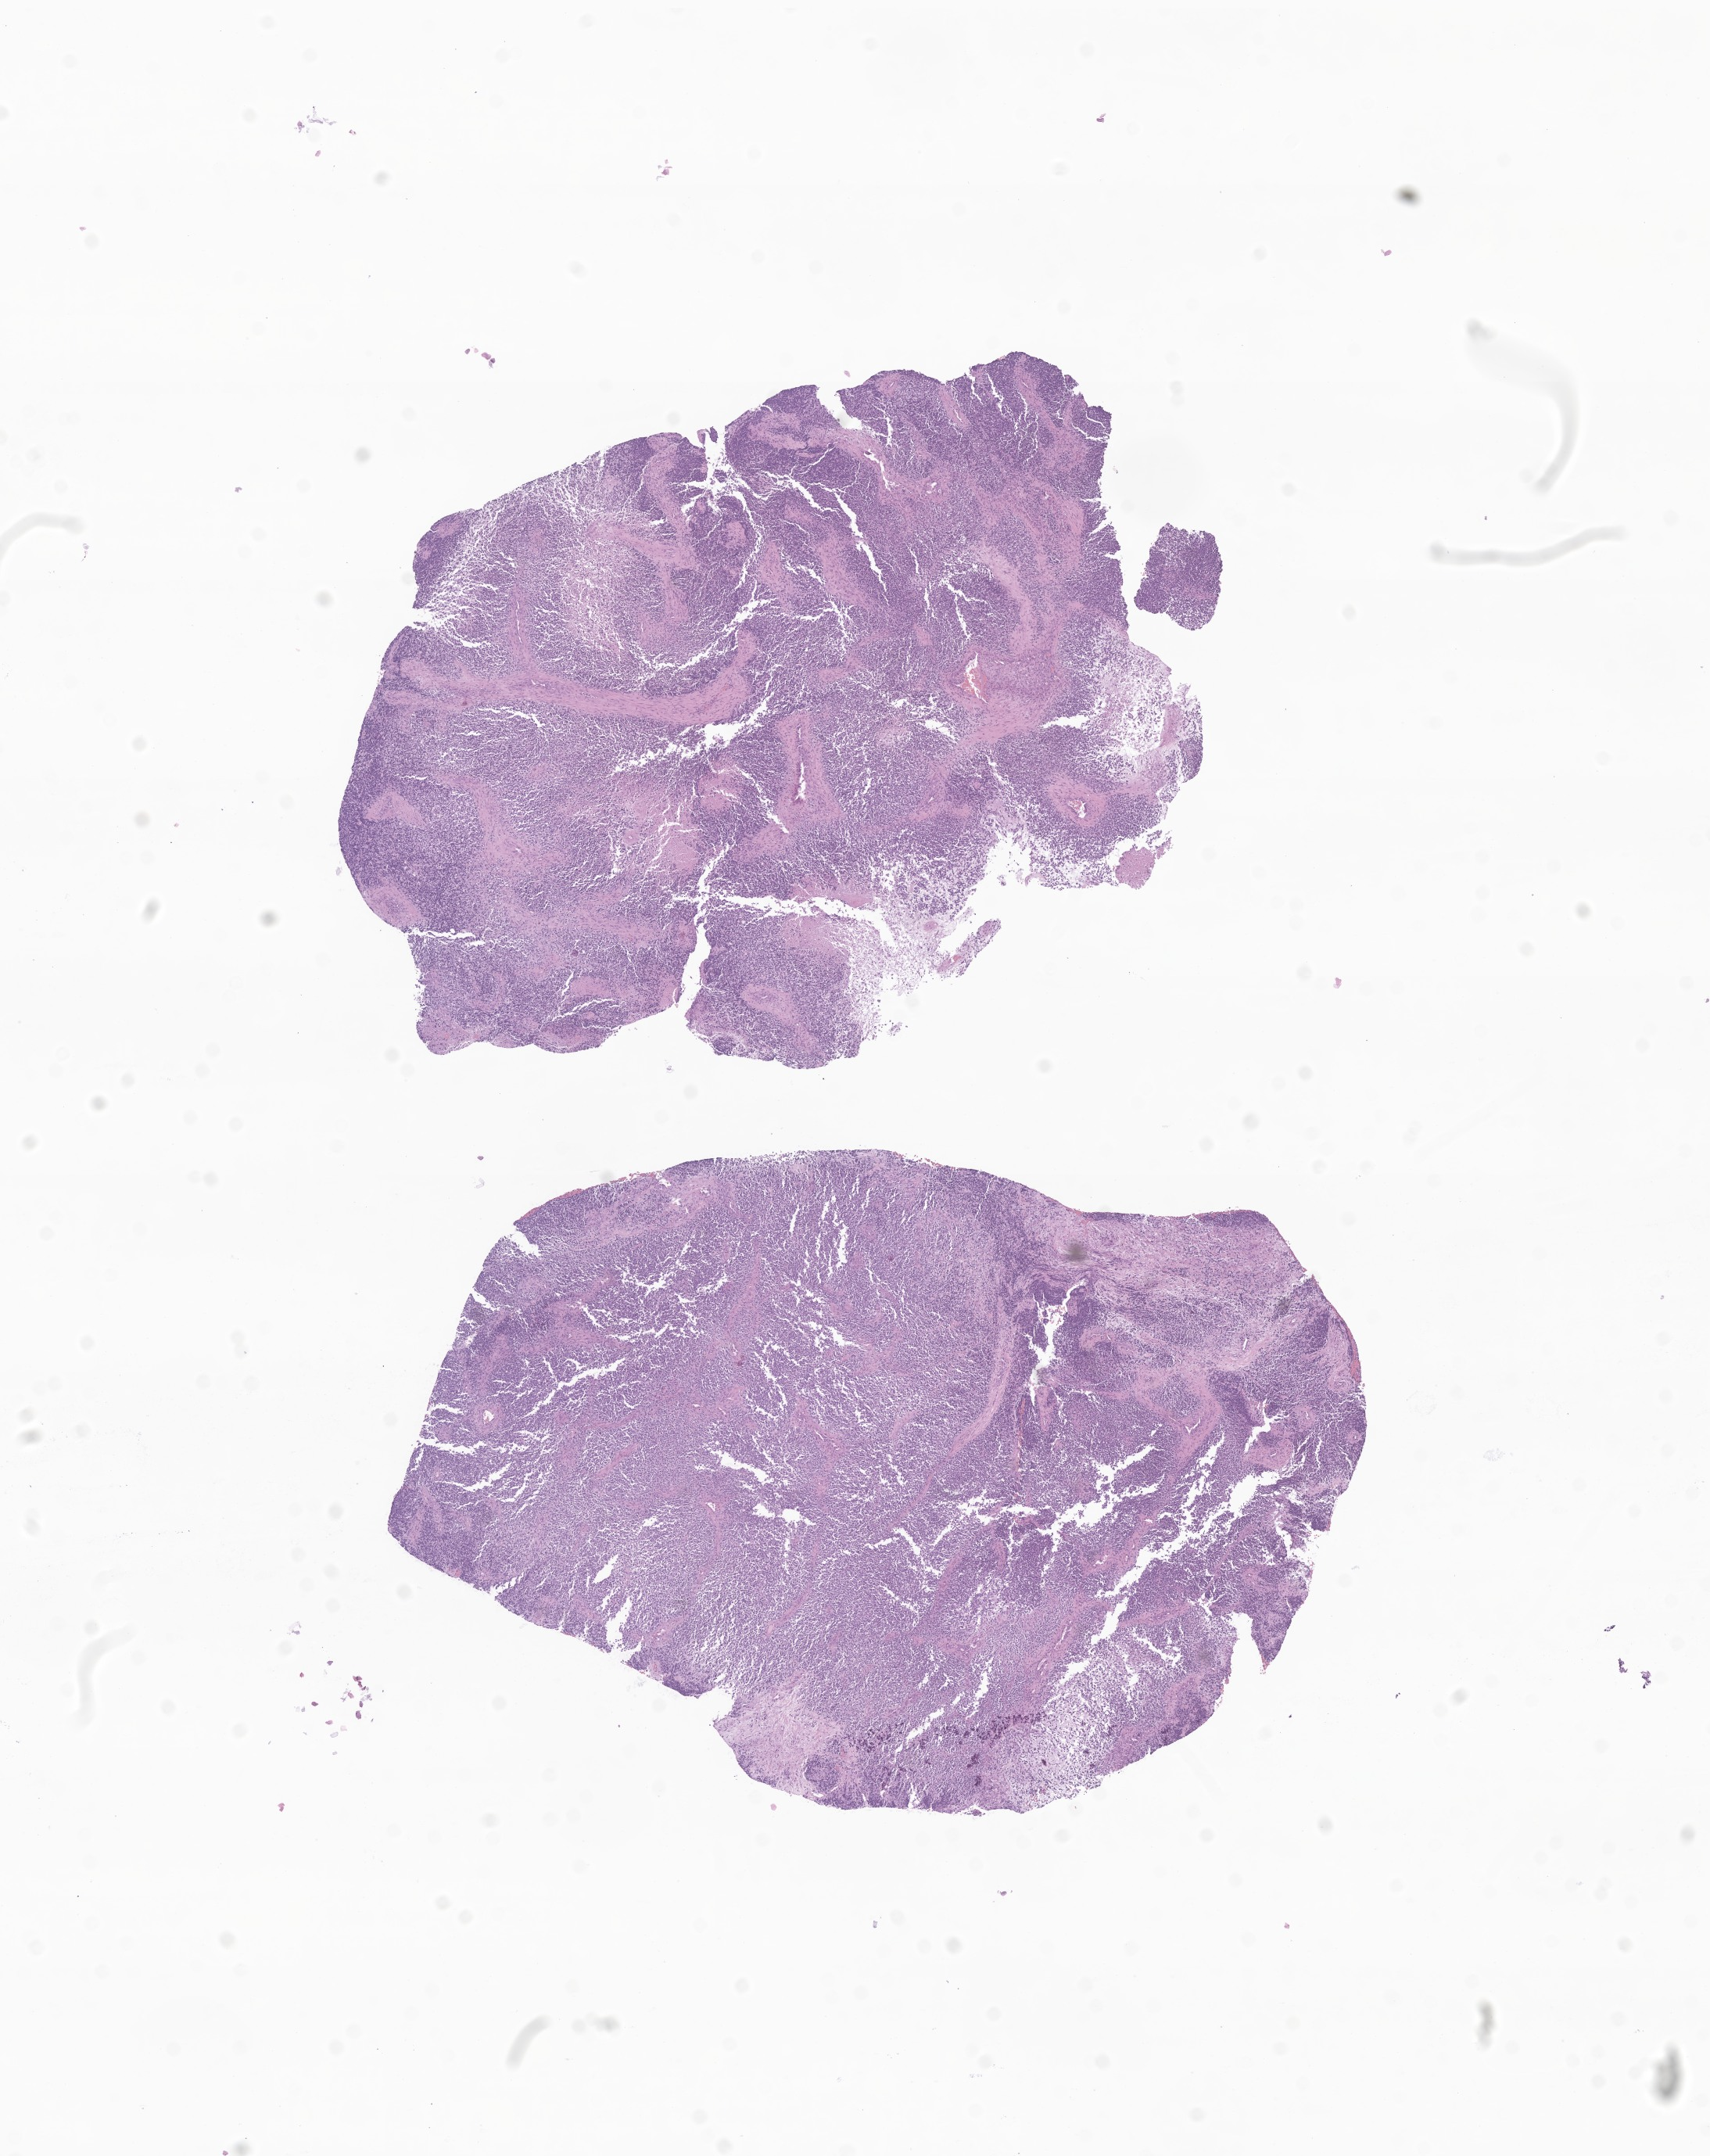
Whole-slide image, haematoxylin and eosin stain of tumor tissue from the orbit — low-resolution overview of the scanned area, about 9.2 x 11.6 mm. Formalin-fixed, paraffin-embedded (FFPE) tissue. Male patient, age 70 months (5 years 10 months).
Recorded diagnosis: Rhabdomyoma, NOS.